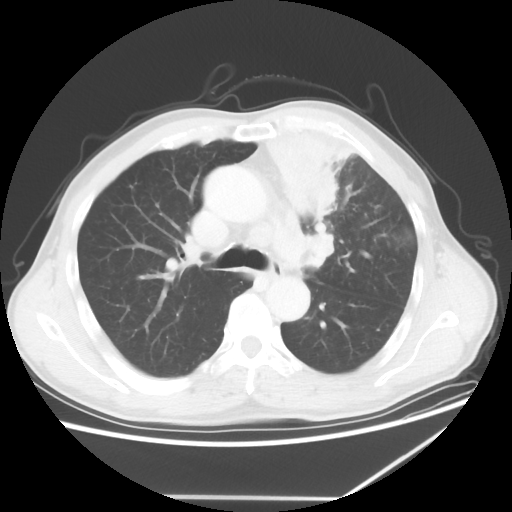
Chest CT, one axial slice; position 41 of 64 along the scan axis; reconstruction kernel STANDARD; lung window (W 1500 / L -600 HU); 5 mm slice thickness; 512 × 512 image matrix. Patient: male, 64 years. From the clinical record (not read from this slice): clinical TNM (as recorded): T1c N1 M1.
Structures marked on this image (bounding box drawn by a radiologist):
- lung tumour (recorded histology: squamous cell carcinoma): bounding box (x1, y1, x2, y2) in pixels: (255, 123, 381, 256)